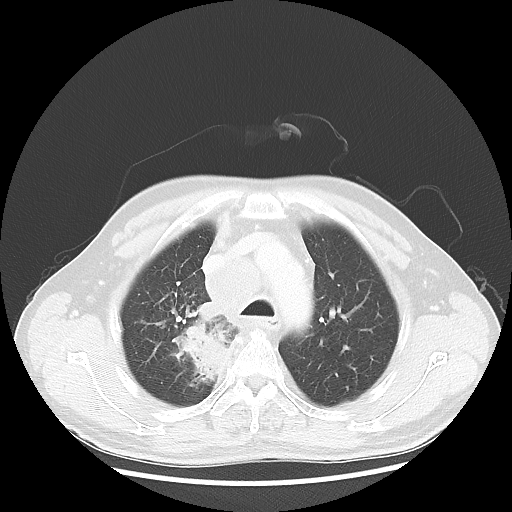
Chest CT, one axial slice; reconstruction kernel LUNG; lung window (W 1500 / L -600 HU); 512 × 512 image matrix. Male patient, age 64 years. Case-level facts recorded for this patient, not image findings: clinical TNM (as recorded): T3 N3 M0.
Annotated regions visible in this slice (rectangle marked by the reading radiologist):
- lung tumour (recorded histology: small cell carcinoma): box from (x=172, y=297) to (x=242, y=386) px